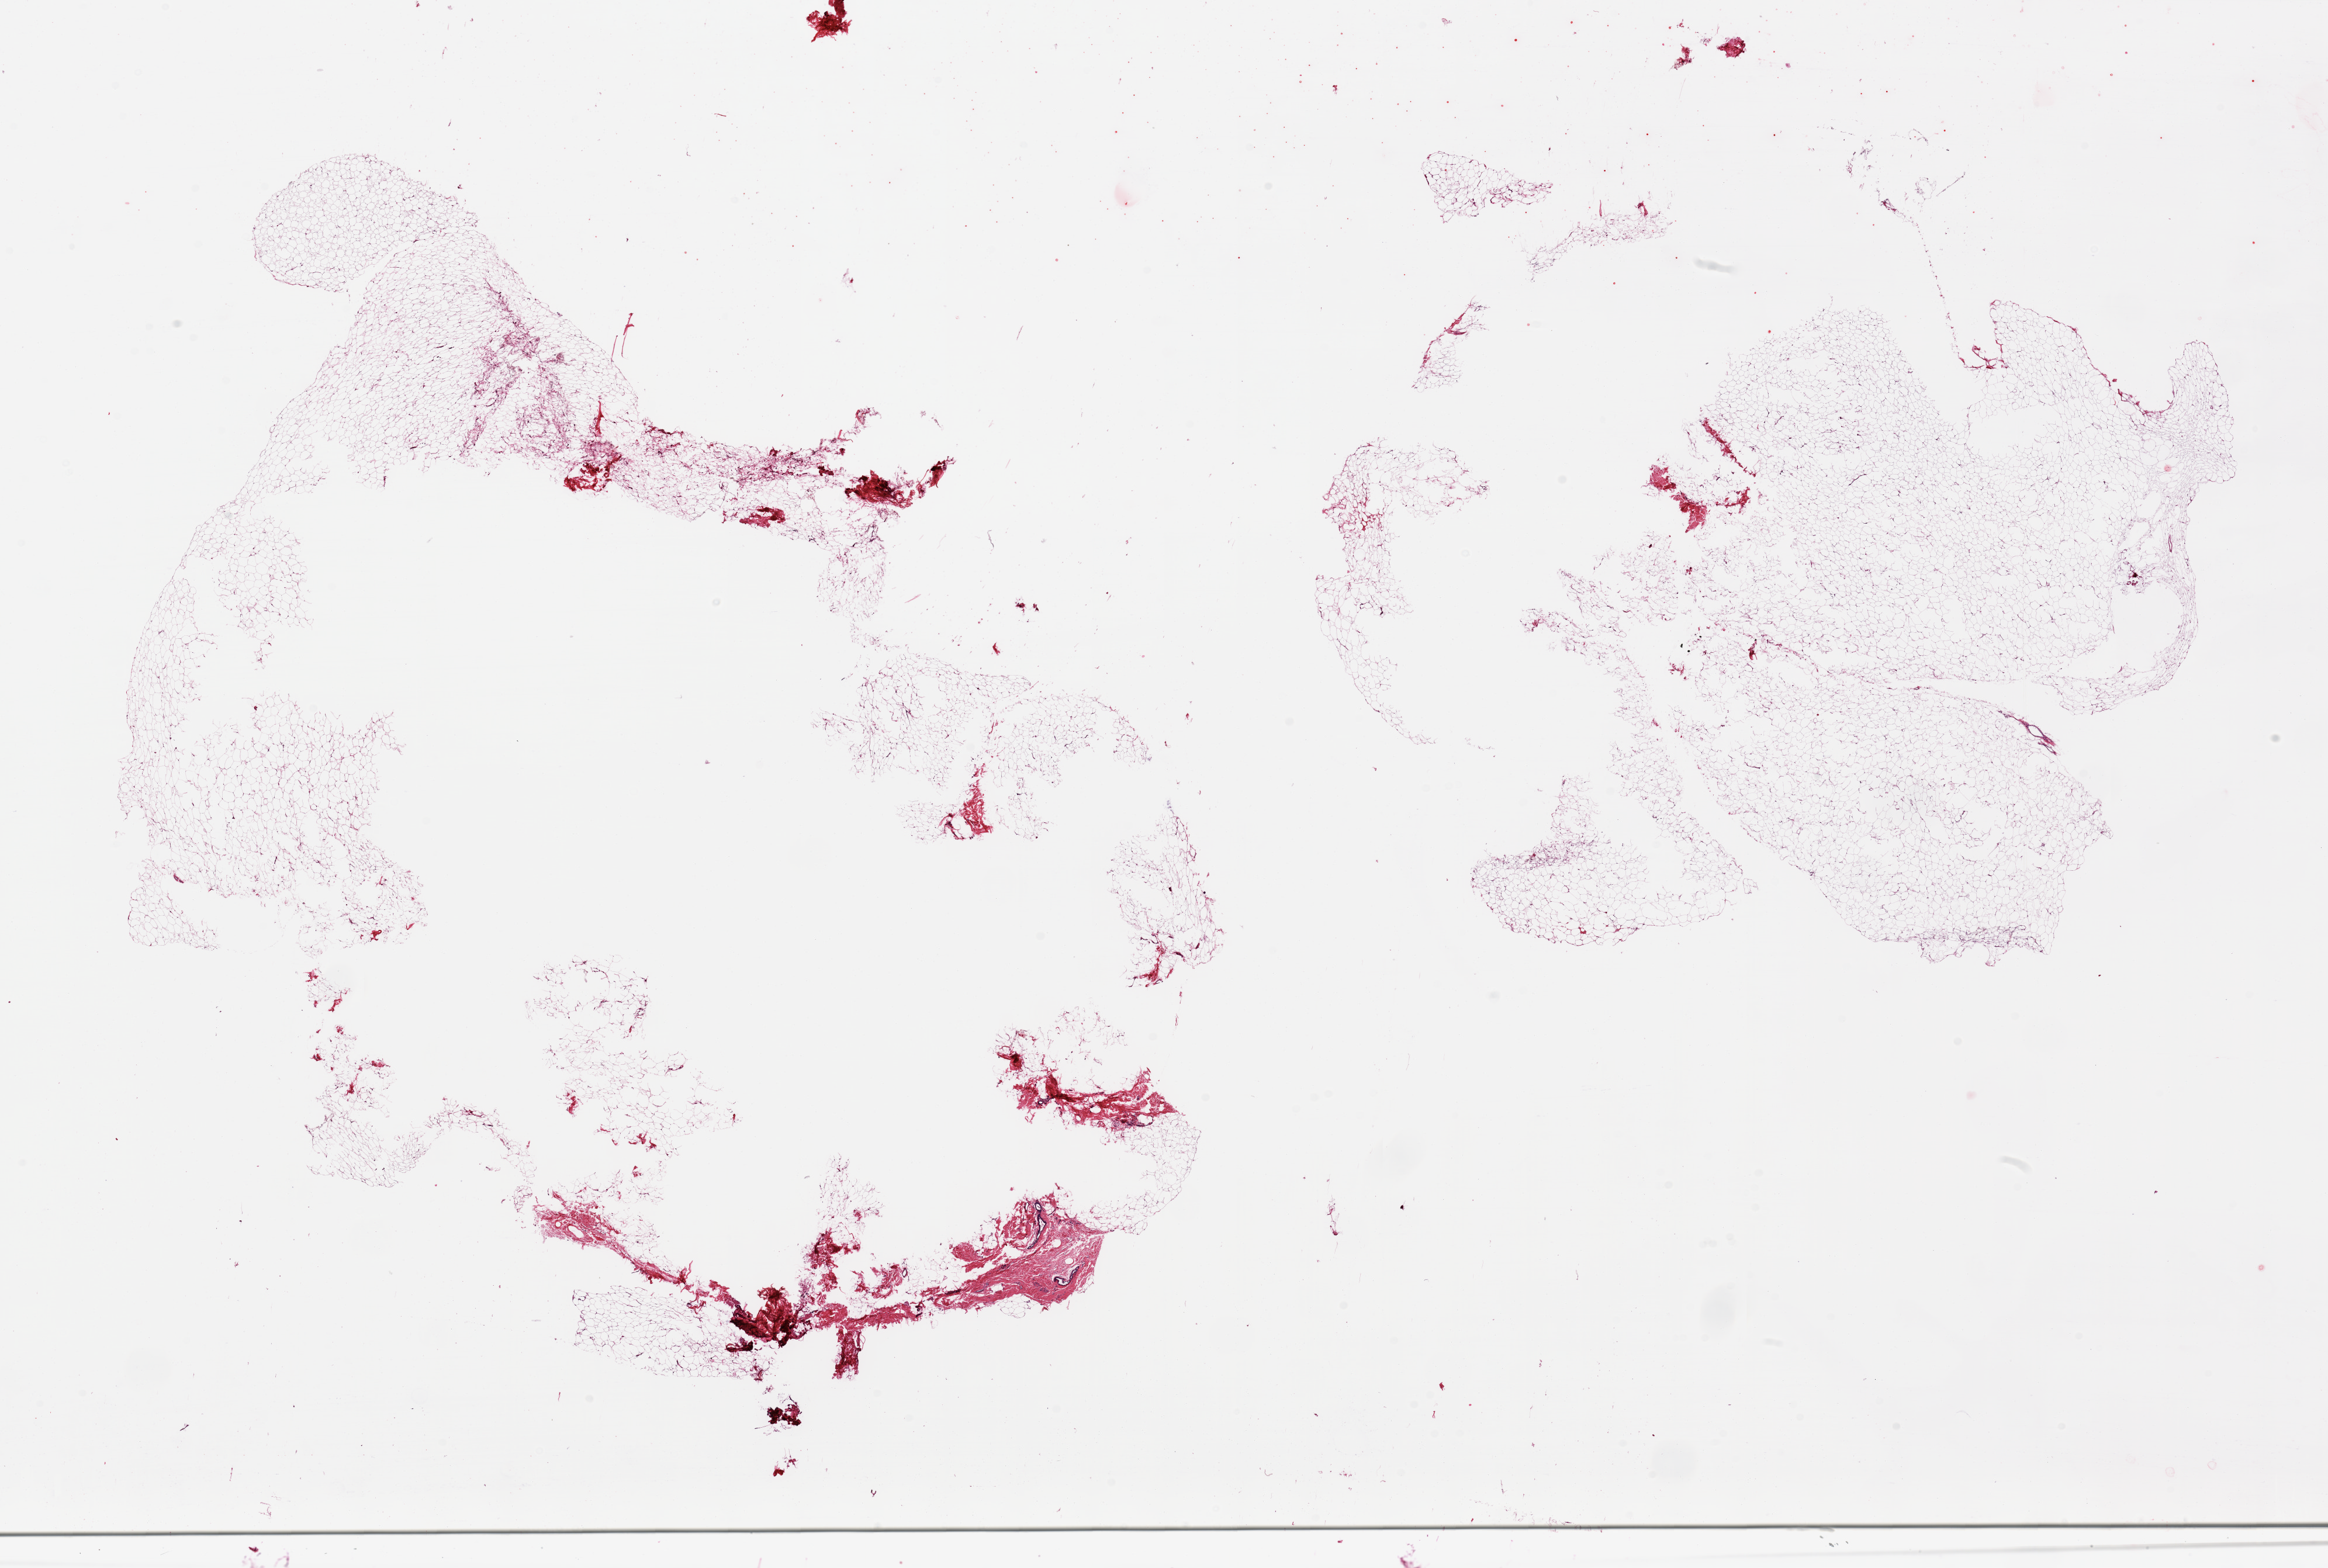
Whole-slide image, haematoxylin and eosin stain, whole scanned area (about 31.5 x 21.2 mm, acquisition: 20x scan) shown as a low-resolution overview, PAXgene-fixed paraffin-embedded (PFPE) section, sampled site (target tissue): breast, tissue donor sample.
• reviewer comment on this tissue sample: 2 pieces; largely fat; few ducts in fibrous component